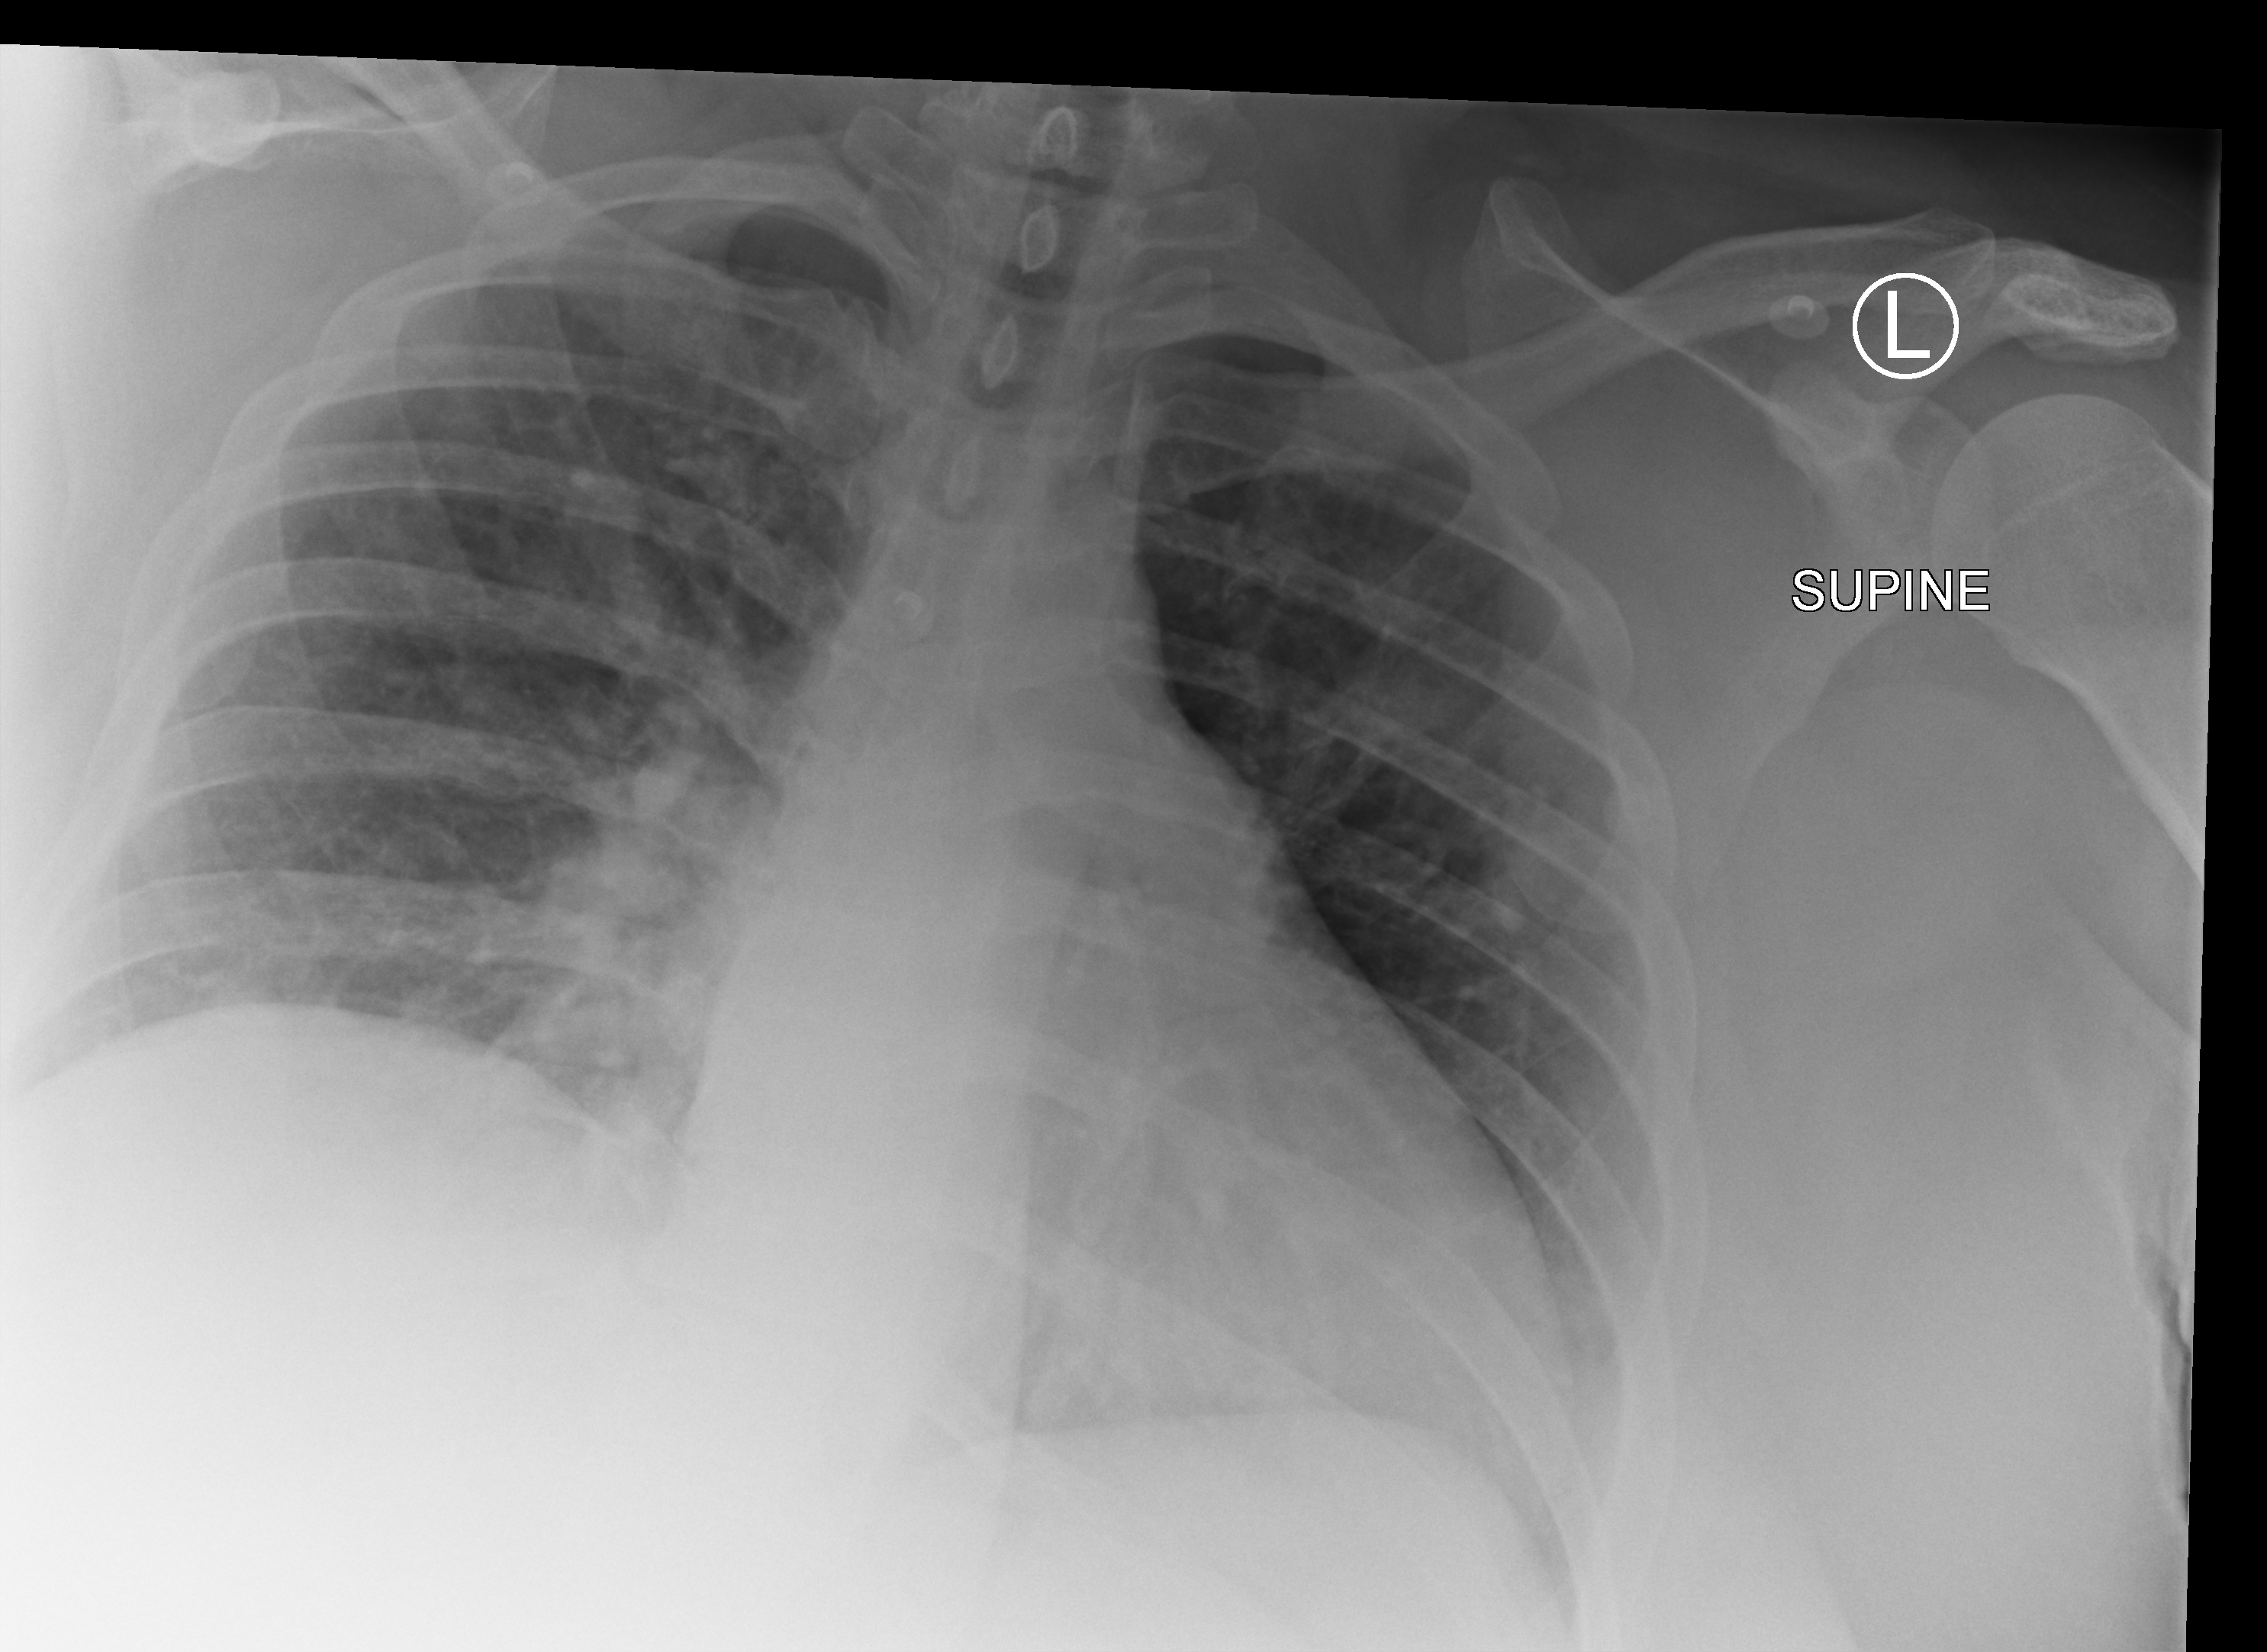
Bedside chest radiograph (computed radiography), anteroposterior (AP) projection. Patient hospitalised with COVID-19; female, aged 18–59 years.
Hospital-stay facts (about this admission, not read from this image; timing relative to this image not recorded):
- admitted to intensive care during this hospital stay: no
- hypertension (admission record): yes
- chronic kidney disease (admission record): no